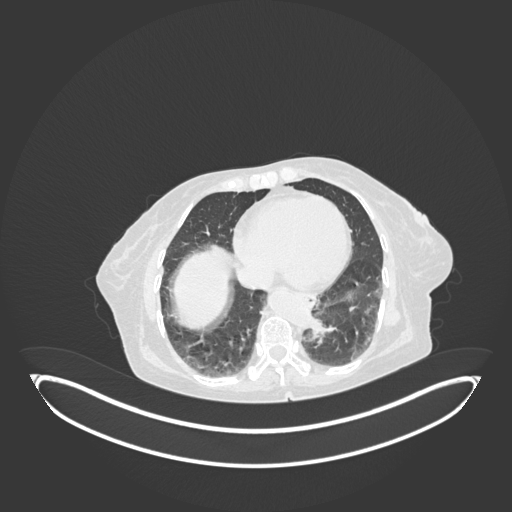
Chest CT, one axial slice. Position 20 of 189 along the scan axis. 120 kVp. Lung window (W 1500 / L -600 HU). 1 mm slice thickness. 512 × 512 image matrix. Patient: female, 82 years. Case-level facts recorded for this patient, not image findings: clinical TNM (as recorded): T1b N0 M1.
Outlined on this slice (rectangle marked by the reading radiologist):
- lung tumour (recorded histology: adenocarcinoma): bounding box [x1, y1, x2, y2] px = [302, 311, 337, 343]